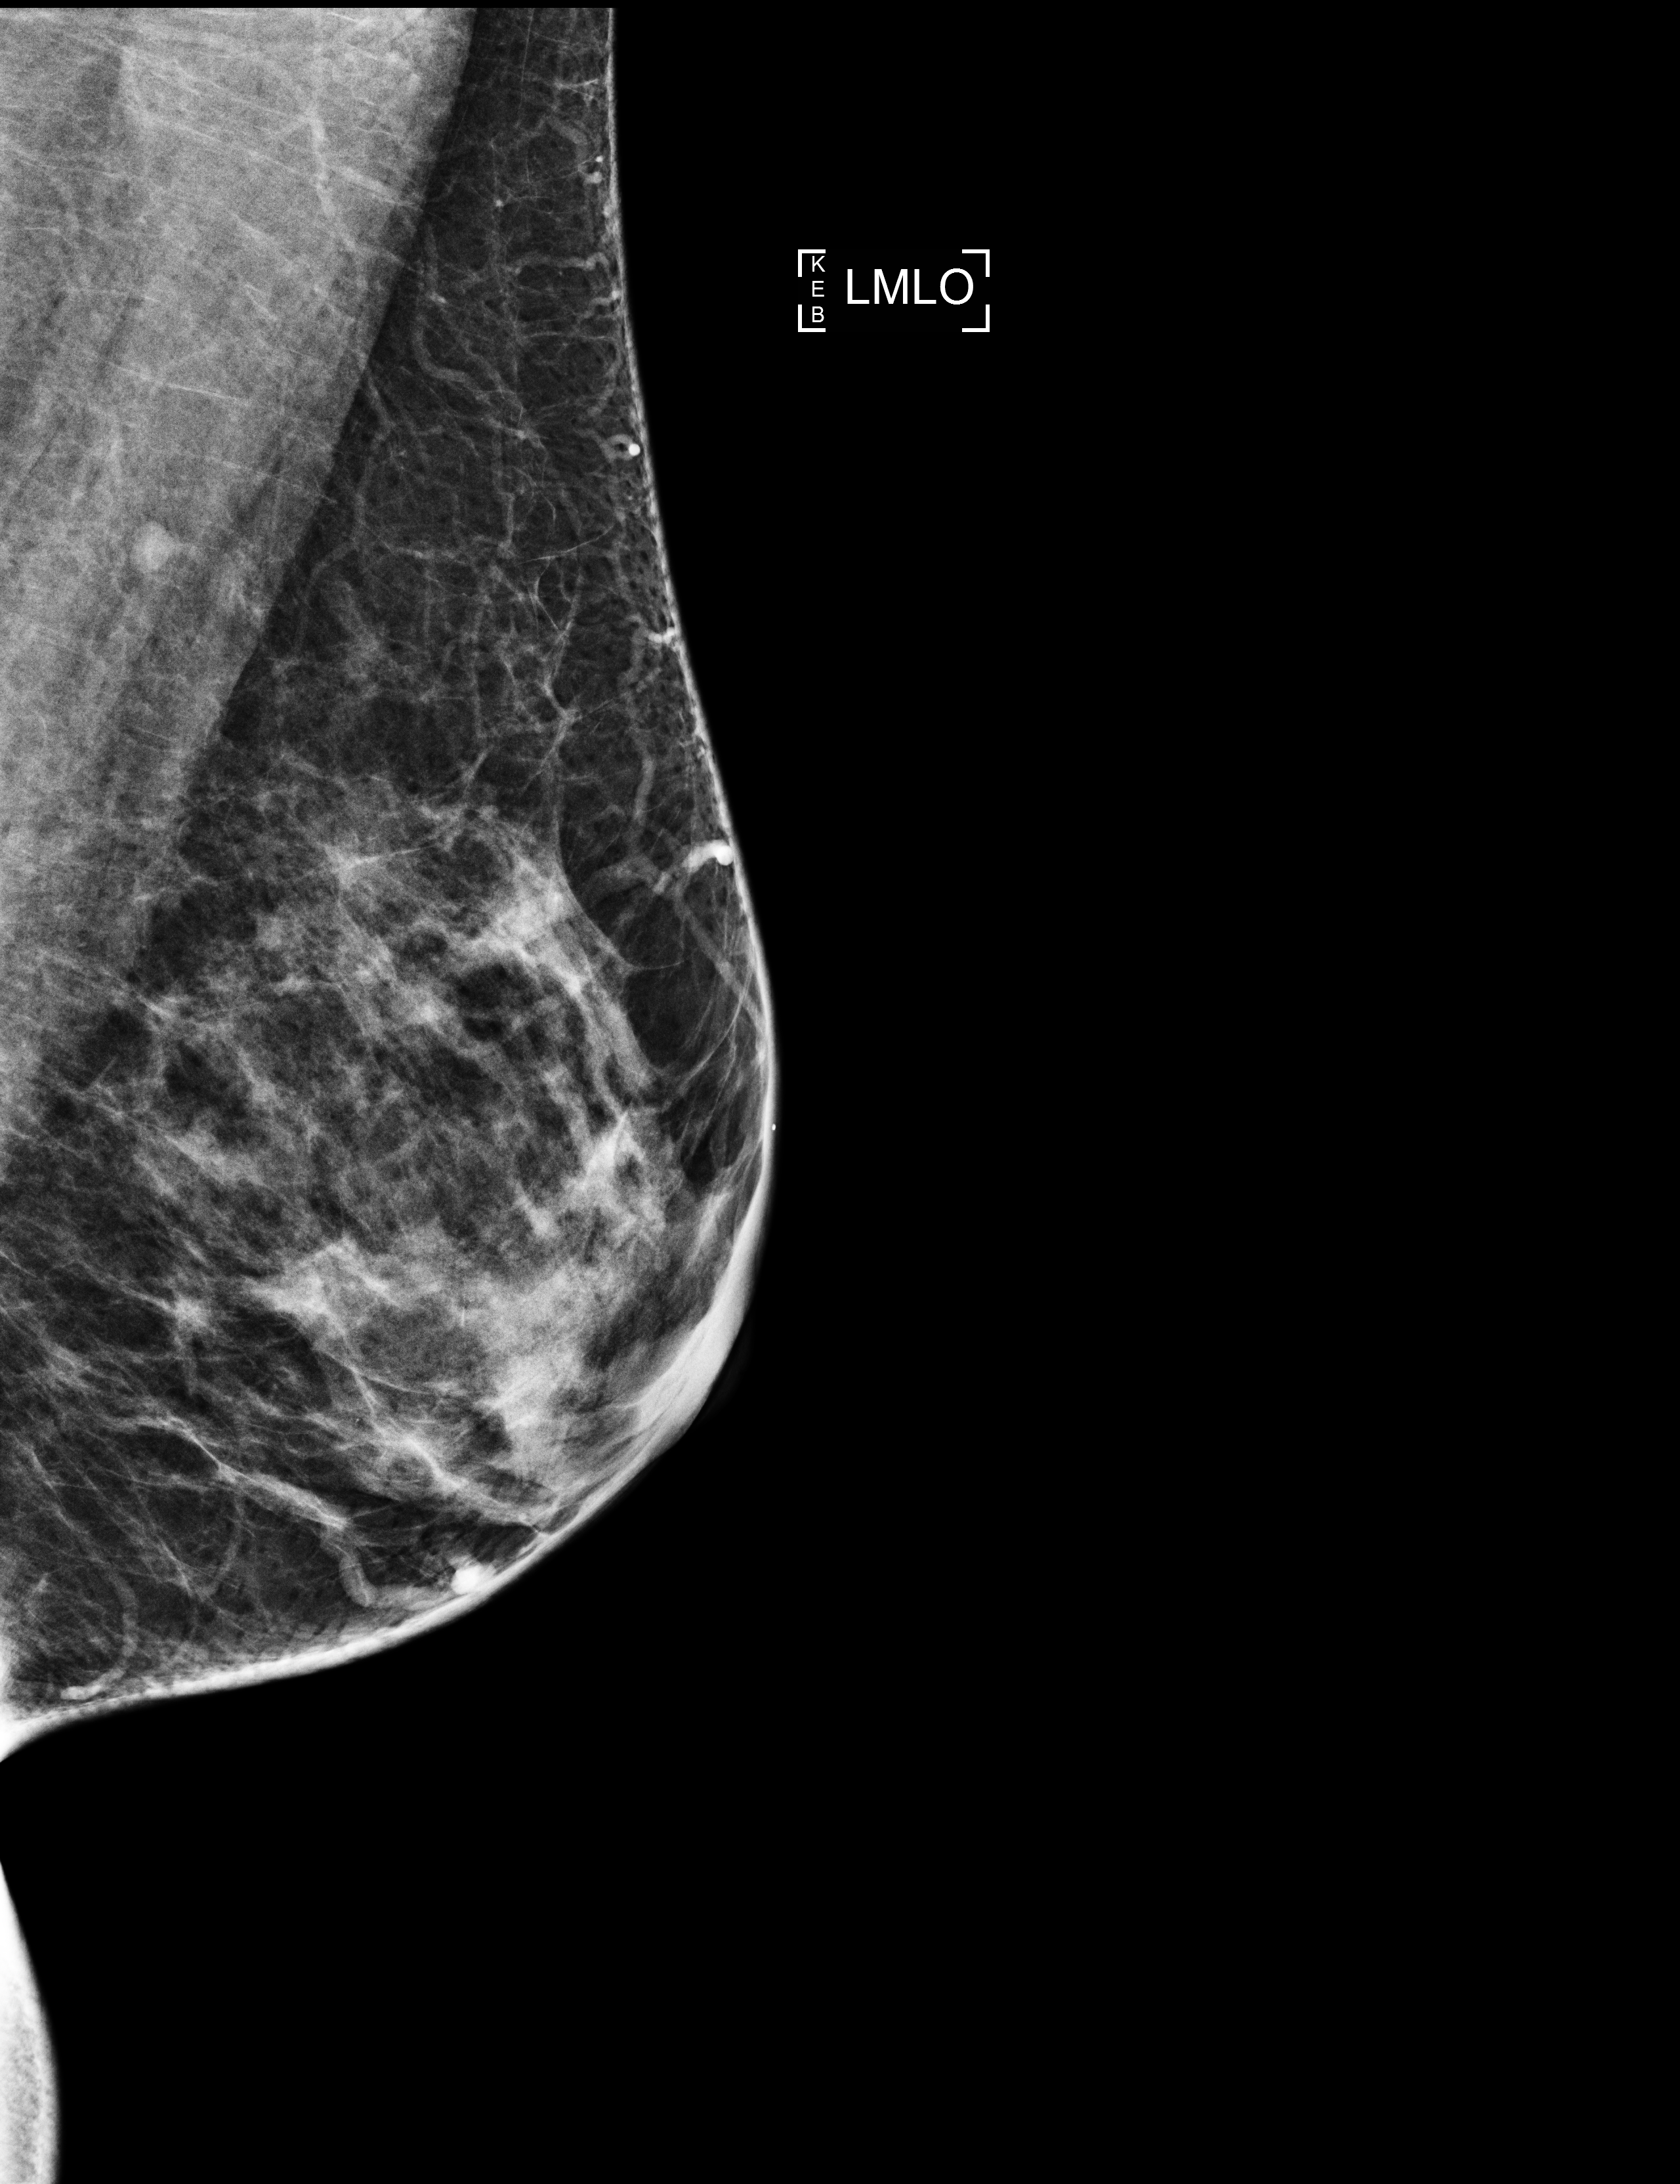
Full-field digital mammogram (FFDM); left breast; mediolateral oblique (MLO) view; screening examination; compressed breast thickness 52 mm; system: Selenia Dimensions. Patient: female, 44 years.
BI-RADS breast density category at the screening exam (both breasts, scale 1–4): 3. Final BI-RADS category for the screening round (tomosynthesis exam, both breasts): category 2. Recall: no recall after this screen.